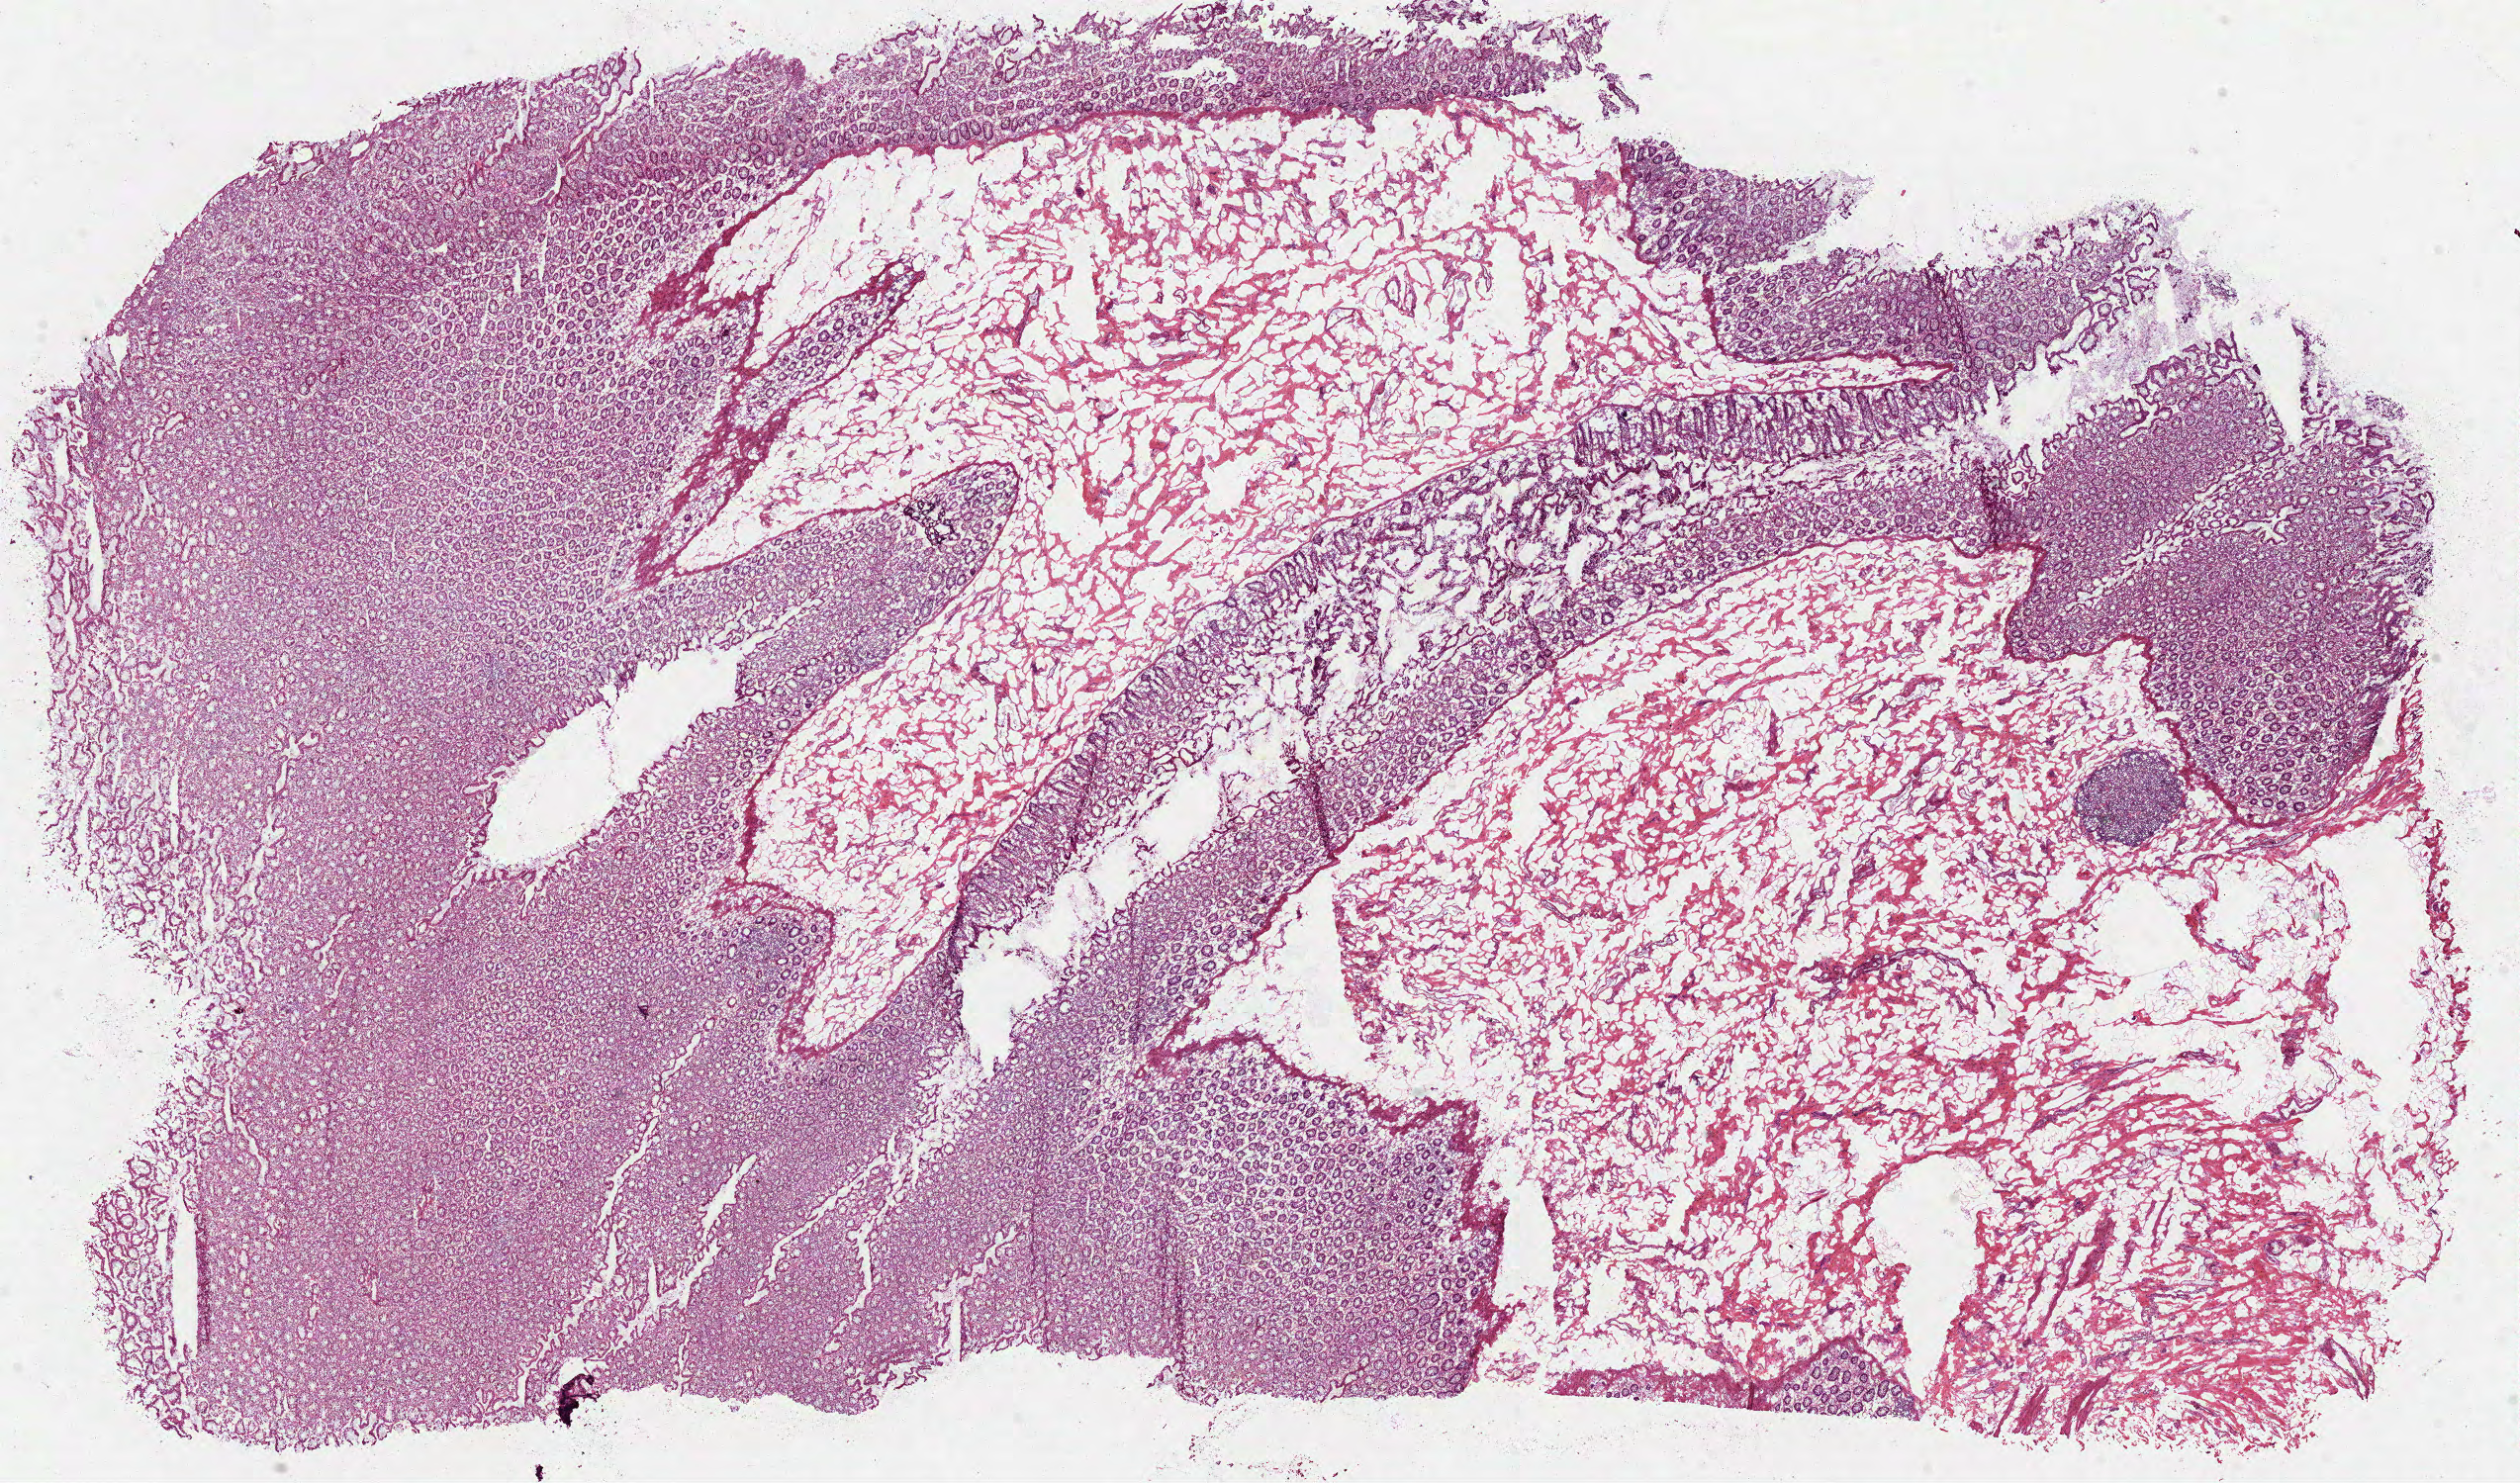
Whole-slide histology image, H&E — whole scanned area (about 20.5 x 12.1 mm, acquisition: 40x scan) shown as a low-resolution overview, frozen section from the top of the tissue portion, sample: solid tissue normal (non-tumour tissue), colon. Patient: female, age at initial diagnosis 77 years.
This section: solid tissue normal (non-tumour) sample from the same patient. Patient diagnosis: Adenocarcinoma, NOS (ascending colon).